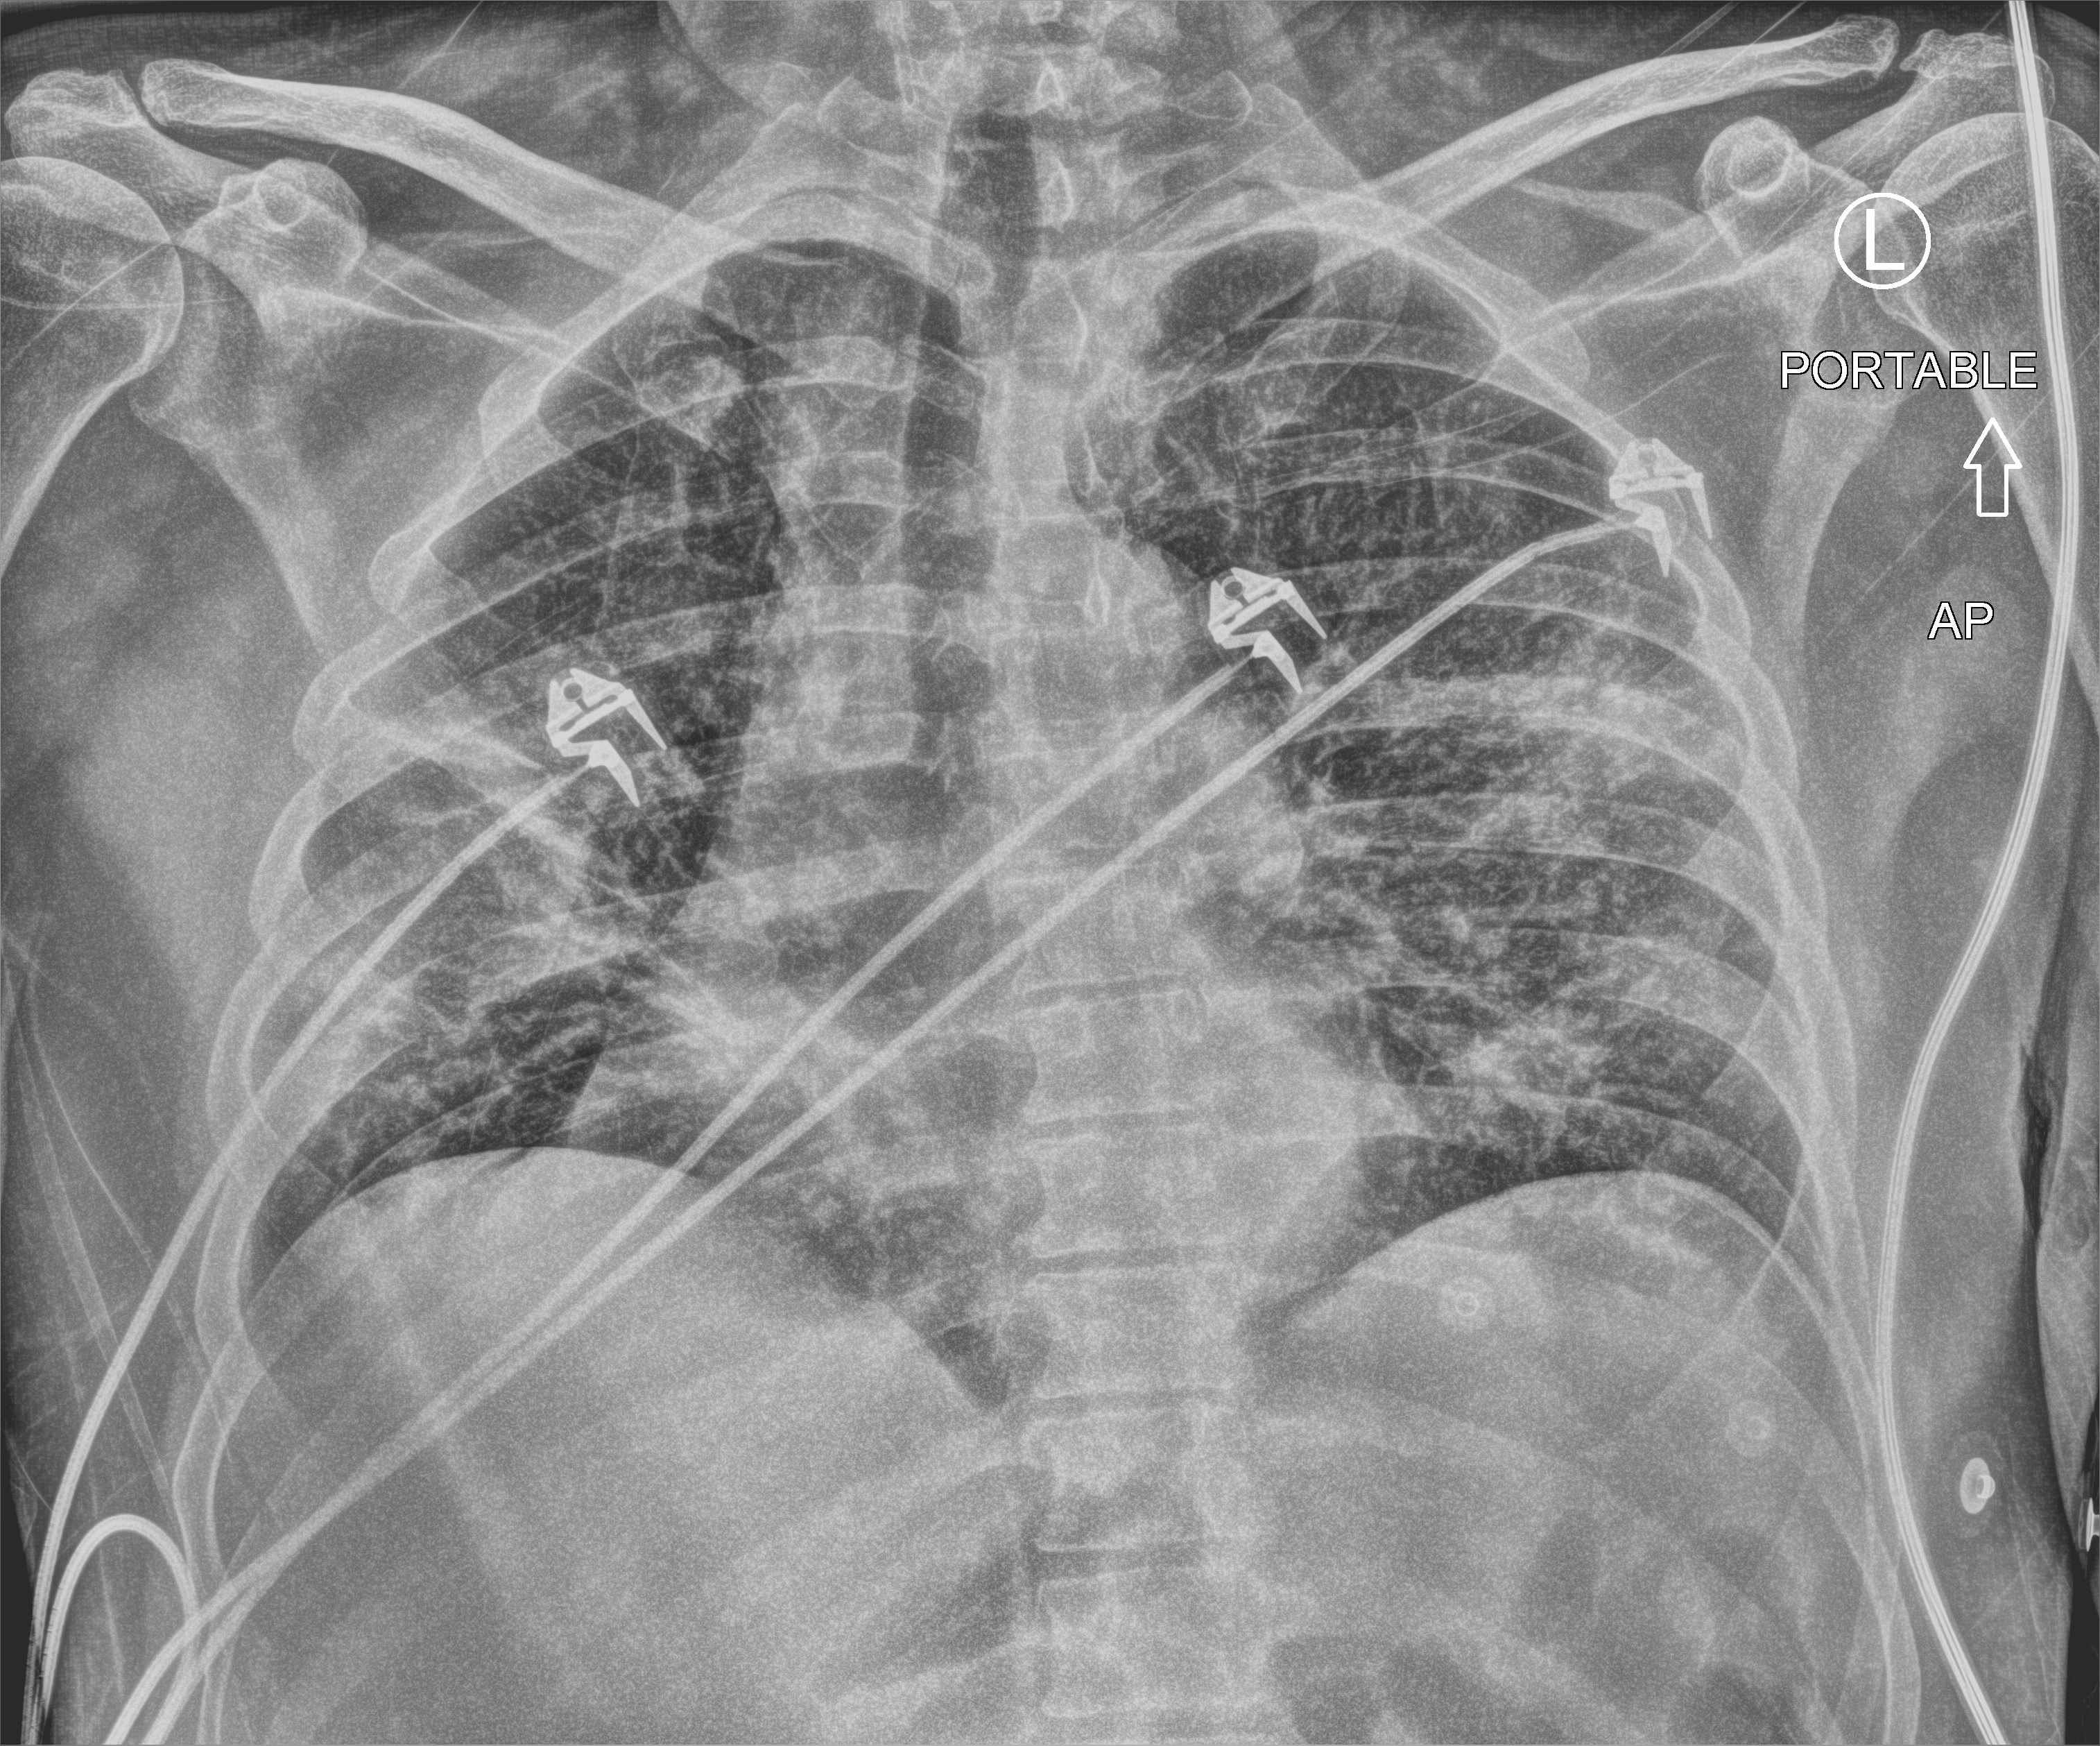
Bedside chest radiograph (computed radiography). Patient hospitalised with COVID-19; male, aged 60–74 years.
Admission-level facts for this patient (not findings on this image; timing relative to this image not recorded):
- length of hospital stay: 11 days
- other chronic lung disease (admission record): no